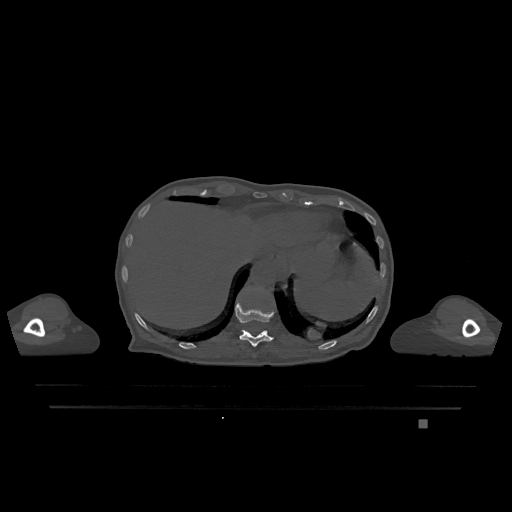
CT including the spine, one axial slice; slice 580 of 1317 in the series (ordered by position); bone window (W 1800 / L 400 HU); 512 × 512 image matrix, field of view 500 × 500 mm. Patient: female, 74 years. From the clinical record (not read from this slice): primary cancer: lung; vertebrae with lytic lesions (as recorded): T1, T4, T5, T6, L4, L5.
Outlined on this slice (semi-automatic segmentation, software-assisted and operator-edited):
- T11 vertebra: bounding box (x1, y1, x2, y2) in pixels: (235, 299, 274, 347)